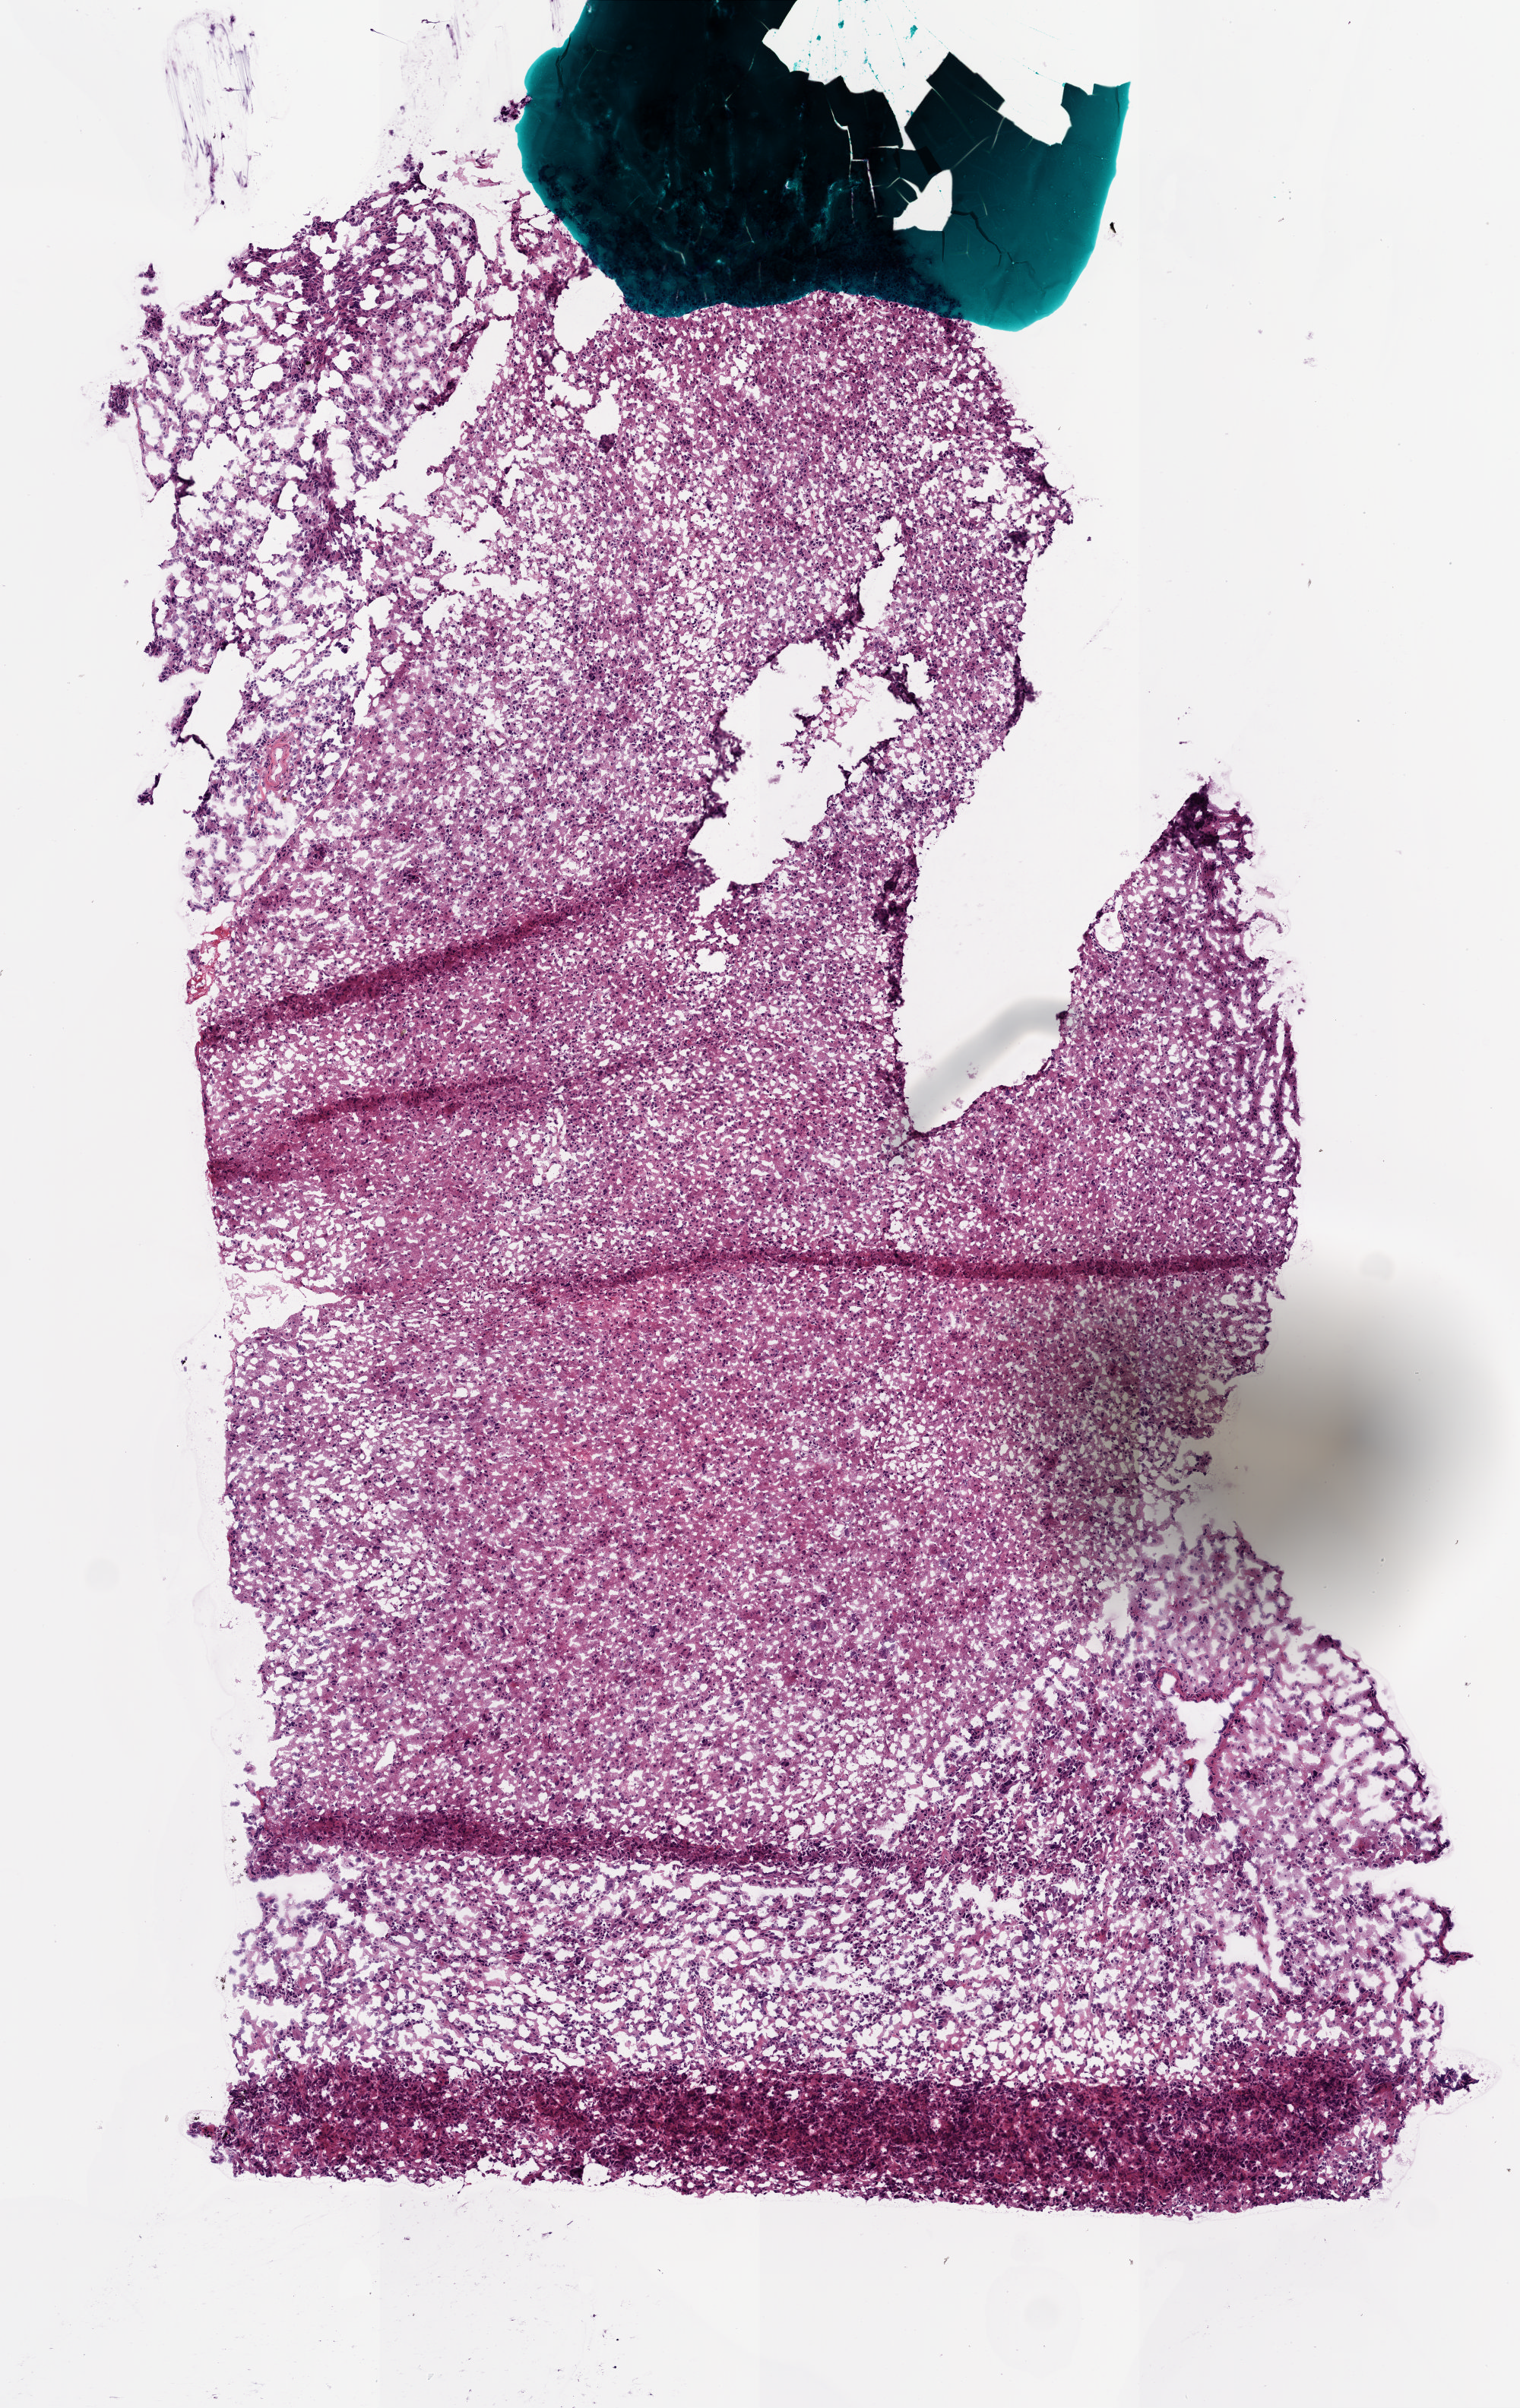
H&E-stained whole-slide image — shown as a low-resolution overview of the whole scanned area (about 4.0 x 6.4 mm, acquisition: 20x scan), frozen section from the bottom of the tissue portion, primary tumour sample from the brain. Male, age 58 years at initial diagnosis. Composition of this section per pathologist review: tumour cells 100%, tumour nuclei 100%, normal cells 0%, stromal cells 0%, necrosis 0%.
* histologic diagnosis: Glioblastoma